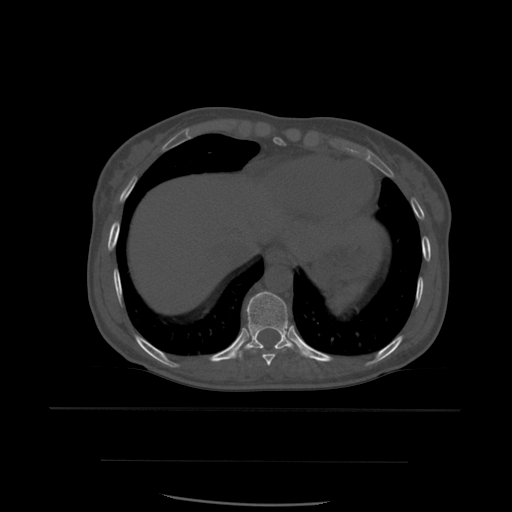
CT including the spine, one axial slice; position 324 of 574 along the scan axis; bone window (W 1800 / L 400 HU); 1.25 mm slice thickness; 512 × 512 image matrix. Patient age 48 years. Case-level facts recorded for this patient, not image findings: primary cancer: lung; vertebrae with lytic lesions (as recorded): T11.
Annotated regions visible in this slice (semi-automatically segmented with operator editing):
- T10 vertebra: bounding box <236,292,304,359> (left, top, right, bottom; pixels)
- T9 vertebra: <244,347,292,366>